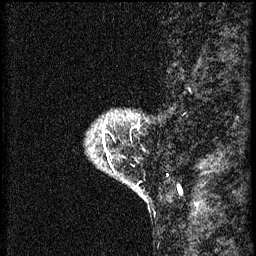
Breast MRI (dynamic contrast-enhanced), one sagittal slice. Slice 7 of 60 in the series (ordered by position). 3 images stored at this slice position (order not interpretable as contrast timing). 1.5 T. TE 4.2 ms, TR 8.2 ms. 2 mm slice thickness. 256 × 256 image matrix, field of view 180 × 180 mm. Female patient, age 41 years.
Structures marked on this image (semi-automatic segmentation, software-assisted and operator-edited):
- analysis volume of interest (the breast-tissue region the enhancement analysis was run in; not a lesion): bounding box <90,114,146,175> (left, top, right, bottom; pixels)
- tumour enhancement mask (voxels above the 70 % enhancement threshold inside the analysis volume of interest): <102,134,108,153>